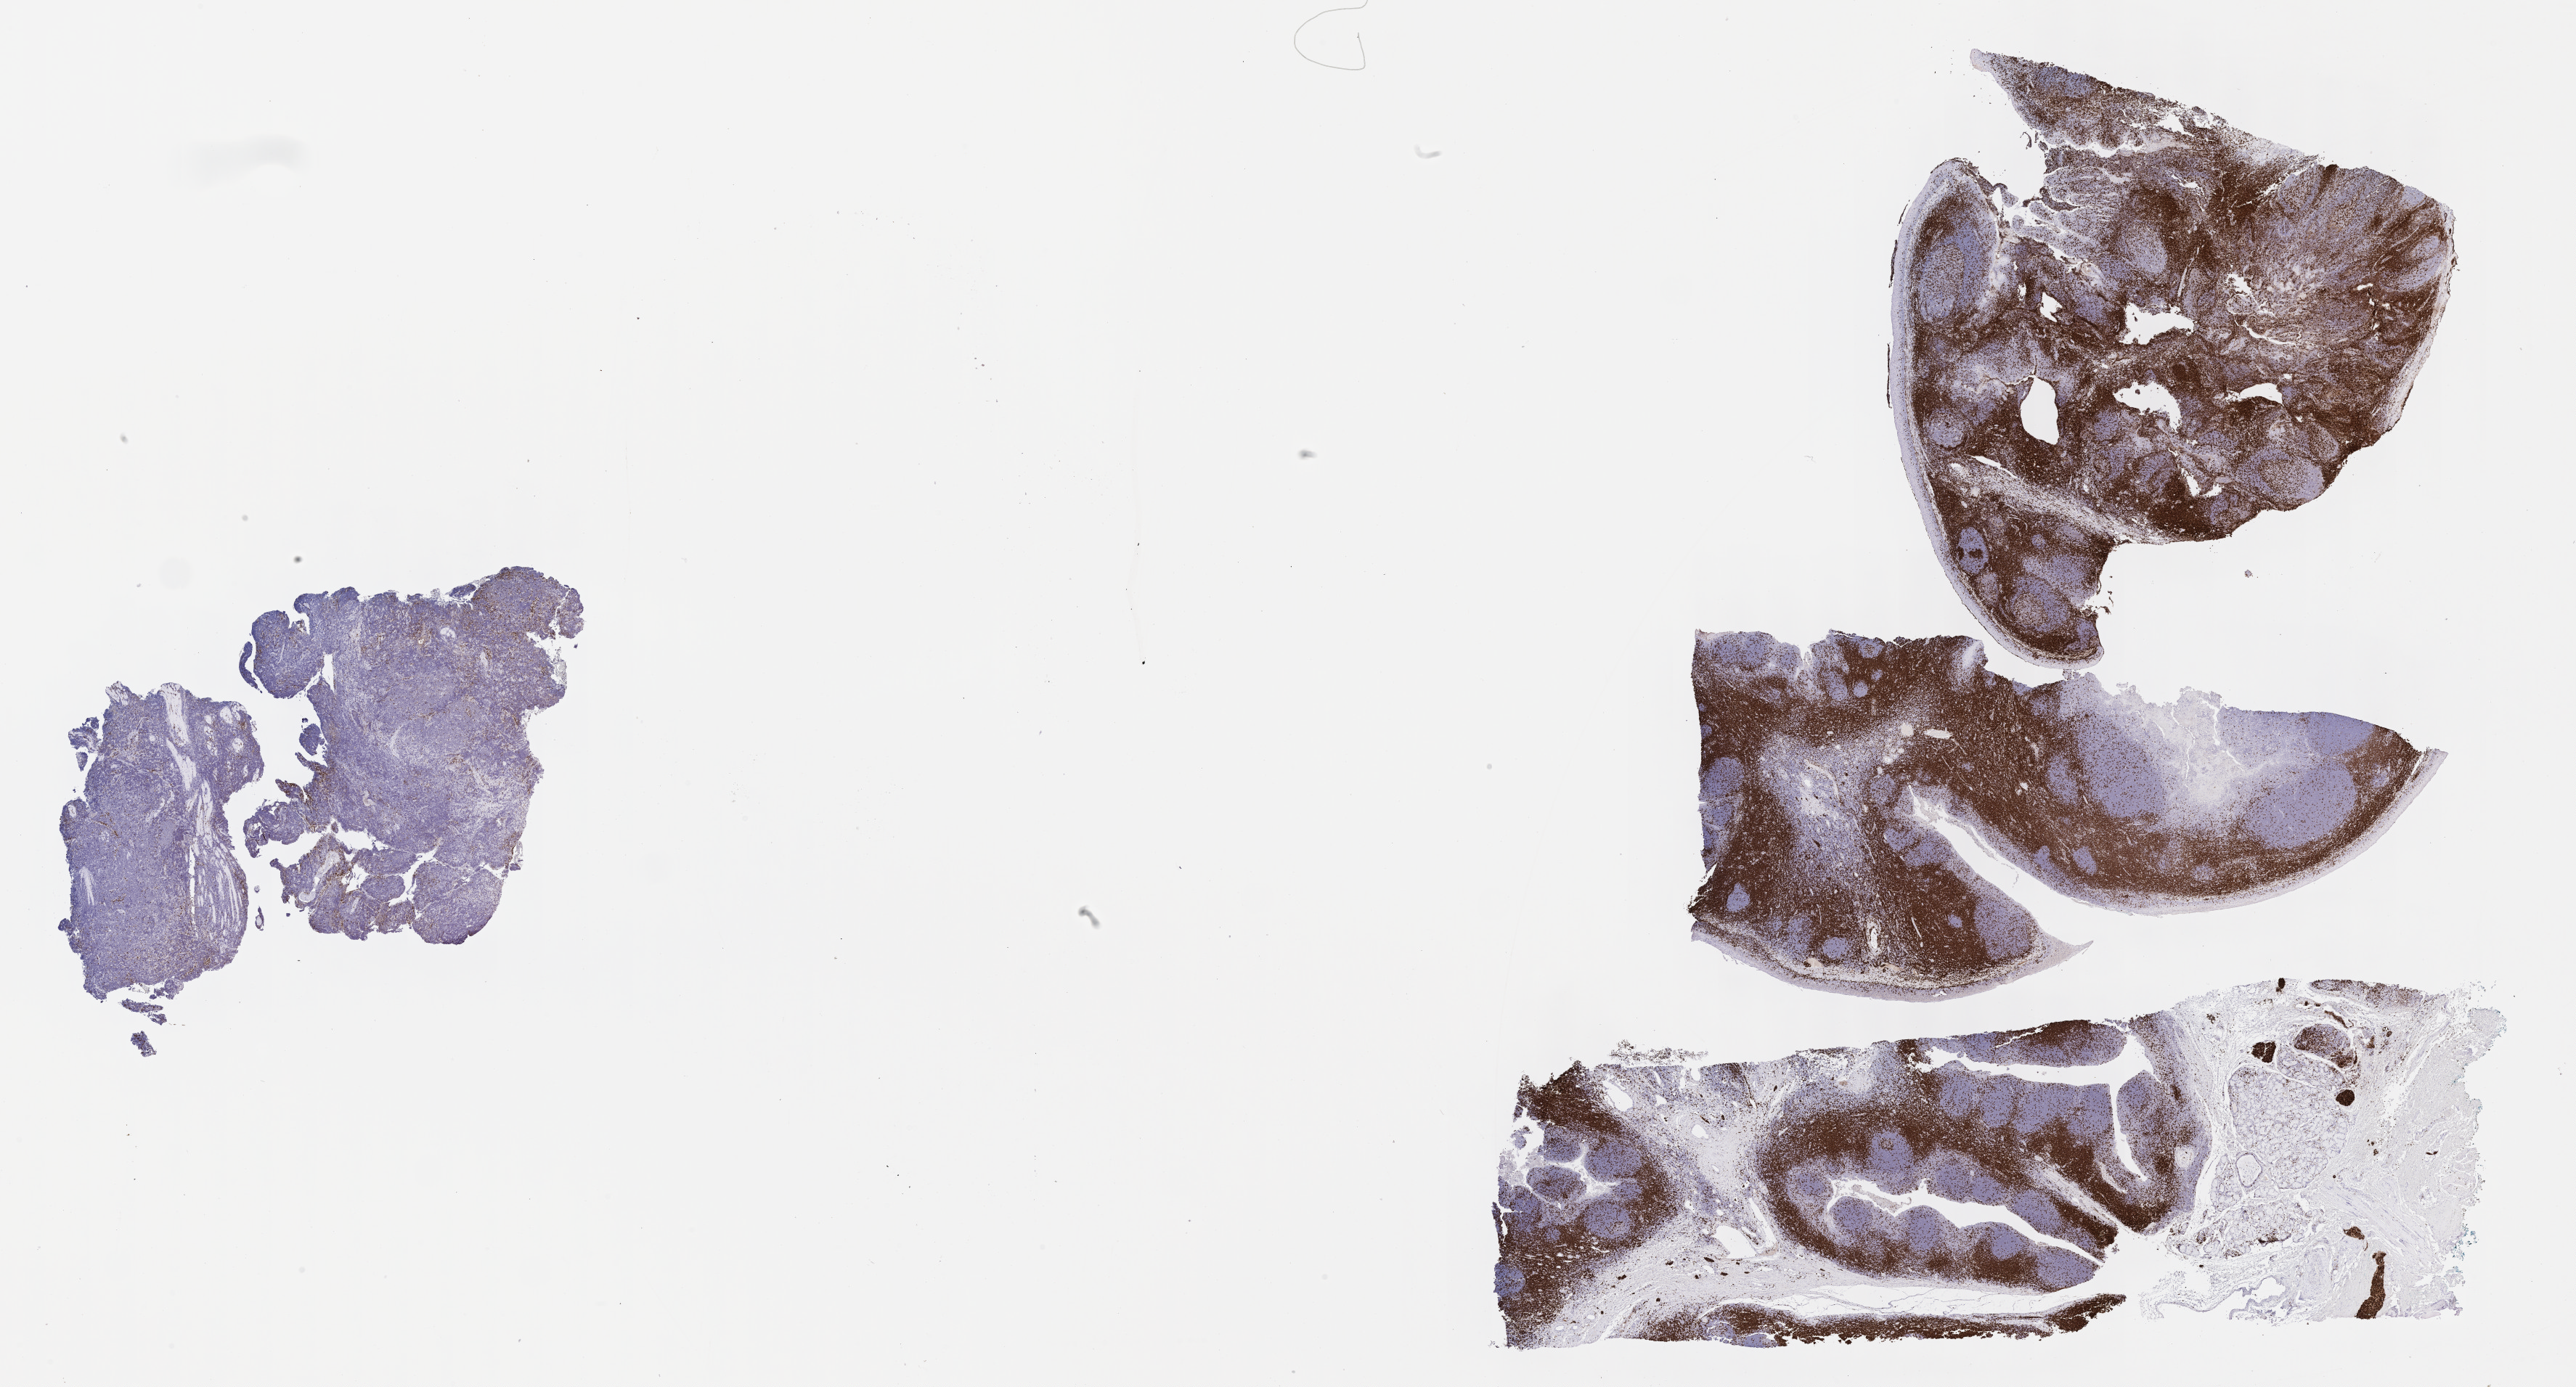
Immunohistochemistry (IHC) whole-slide image stained for CD3, low-resolution overview of the scanned area, about 28.7 x 15.4 mm; specimen: tumor tissue; site: cranium. Male patient; age at initial diagnosis 8 years.
• diagnosis: Burkitt lymphoma, NOS